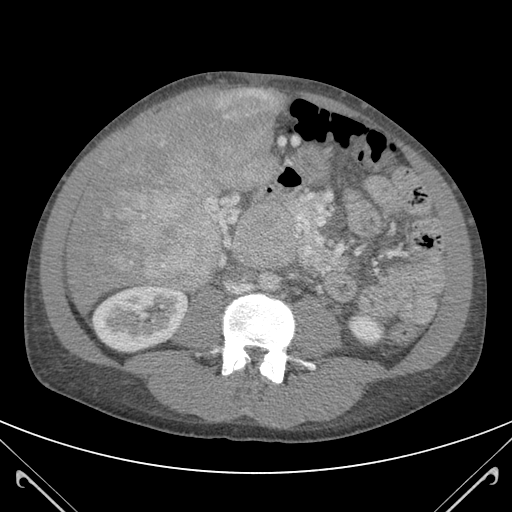
Contrast-enhanced abdominal CT (liver protocol), one axial slice. Position 41 of 118 along the scan axis. 120 kVp. Soft-tissue window (W 400 / L 40 HU). 3 mm slice thickness. 512 × 512 image matrix. From the clinical record (not read from this slice): diagnosis: hepatocellular carcinoma (patient treated with transarterial chemoembolisation; whether this scan precedes or follows treatment is not stated here); TNM stage (as recorded): Stage-IIIB; Child-Pugh class: A; tumour nodularity: uninodular.
Outlined on this slice (semi-automatically segmented with operator editing):
- liver parenchyma outside the tumour (the mass and vessels are separate outlines, so this box may not span the whole liver): bounding box [x1, y1, x2, y2] px = [67, 89, 281, 311]
- mass: [92, 89, 279, 288]
- liver vessels: [147, 273, 151, 275]